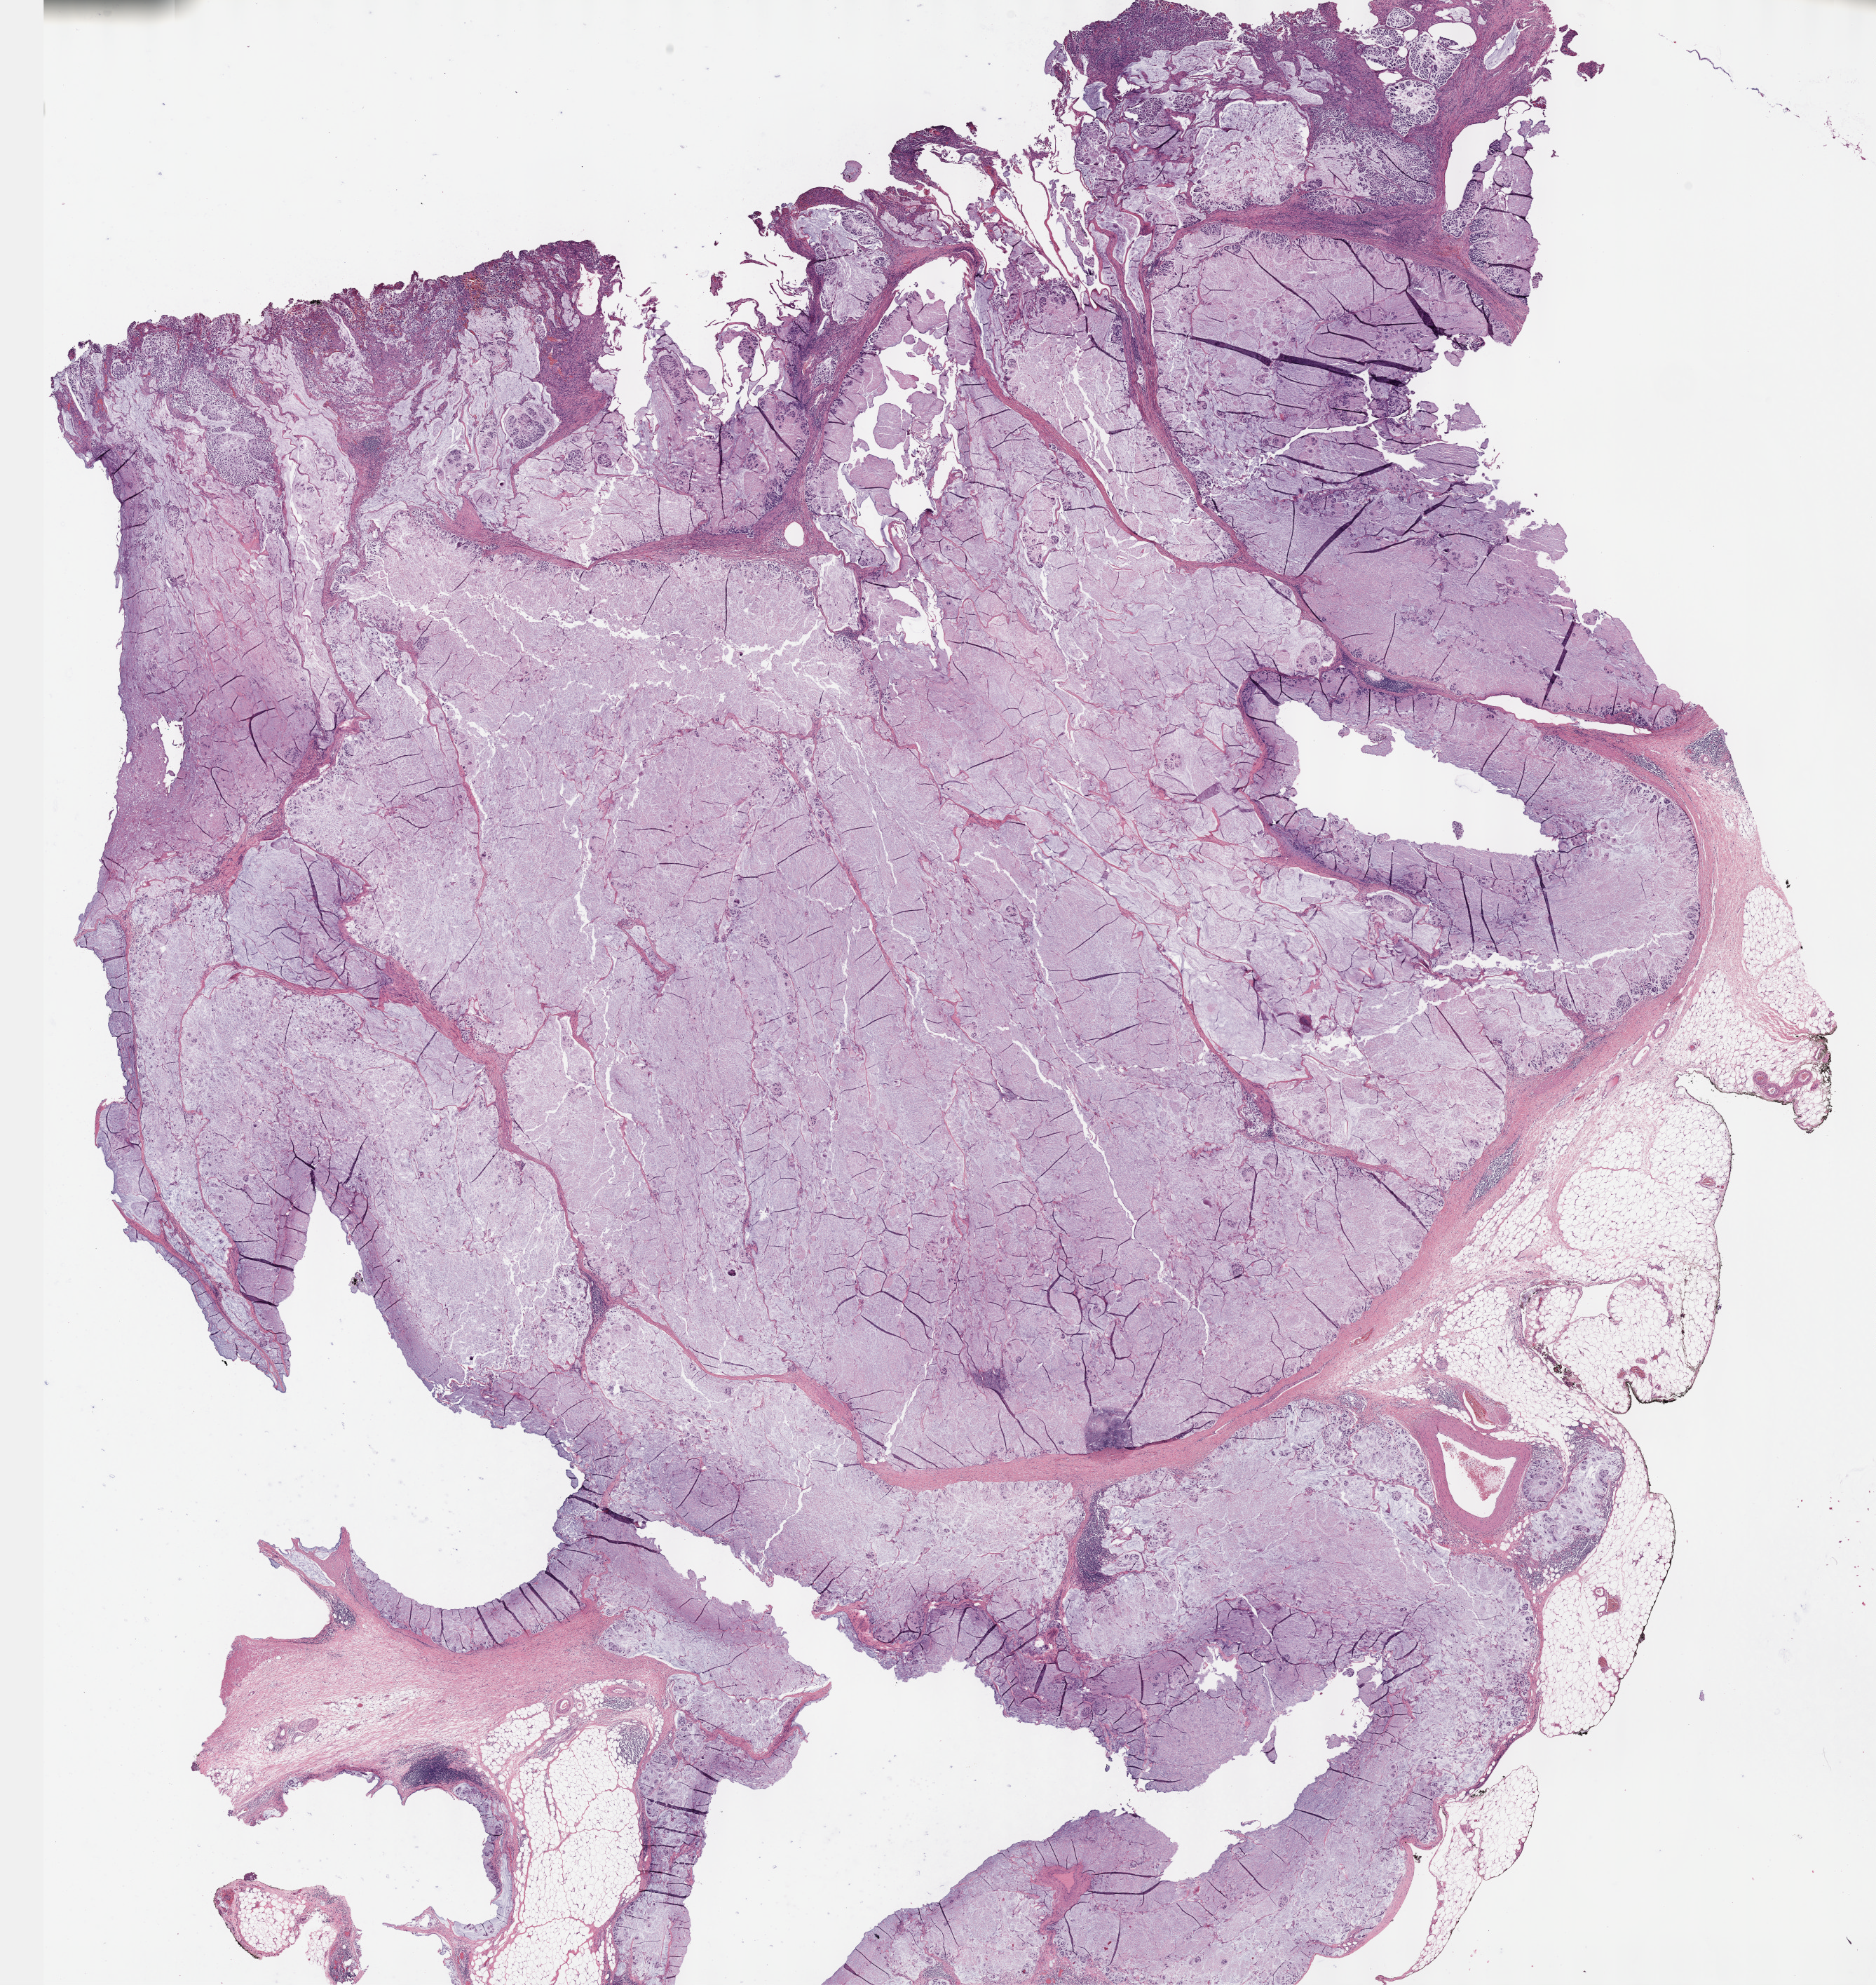
Digitized H&E tissue section (whole slide), low-resolution overview of the scanned area, about 21.6 x 22.9 mm; formalin-fixed paraffin-embedded (FFPE) diagnostic section; stomach, primary tumour sample. Male patient; age at initial diagnosis 67 years. Histologic grade: G1 (well differentiated).
AJCC pathologic stage: IIIB. Diagnosis: Mucinous adenocarcinoma (body of stomach).